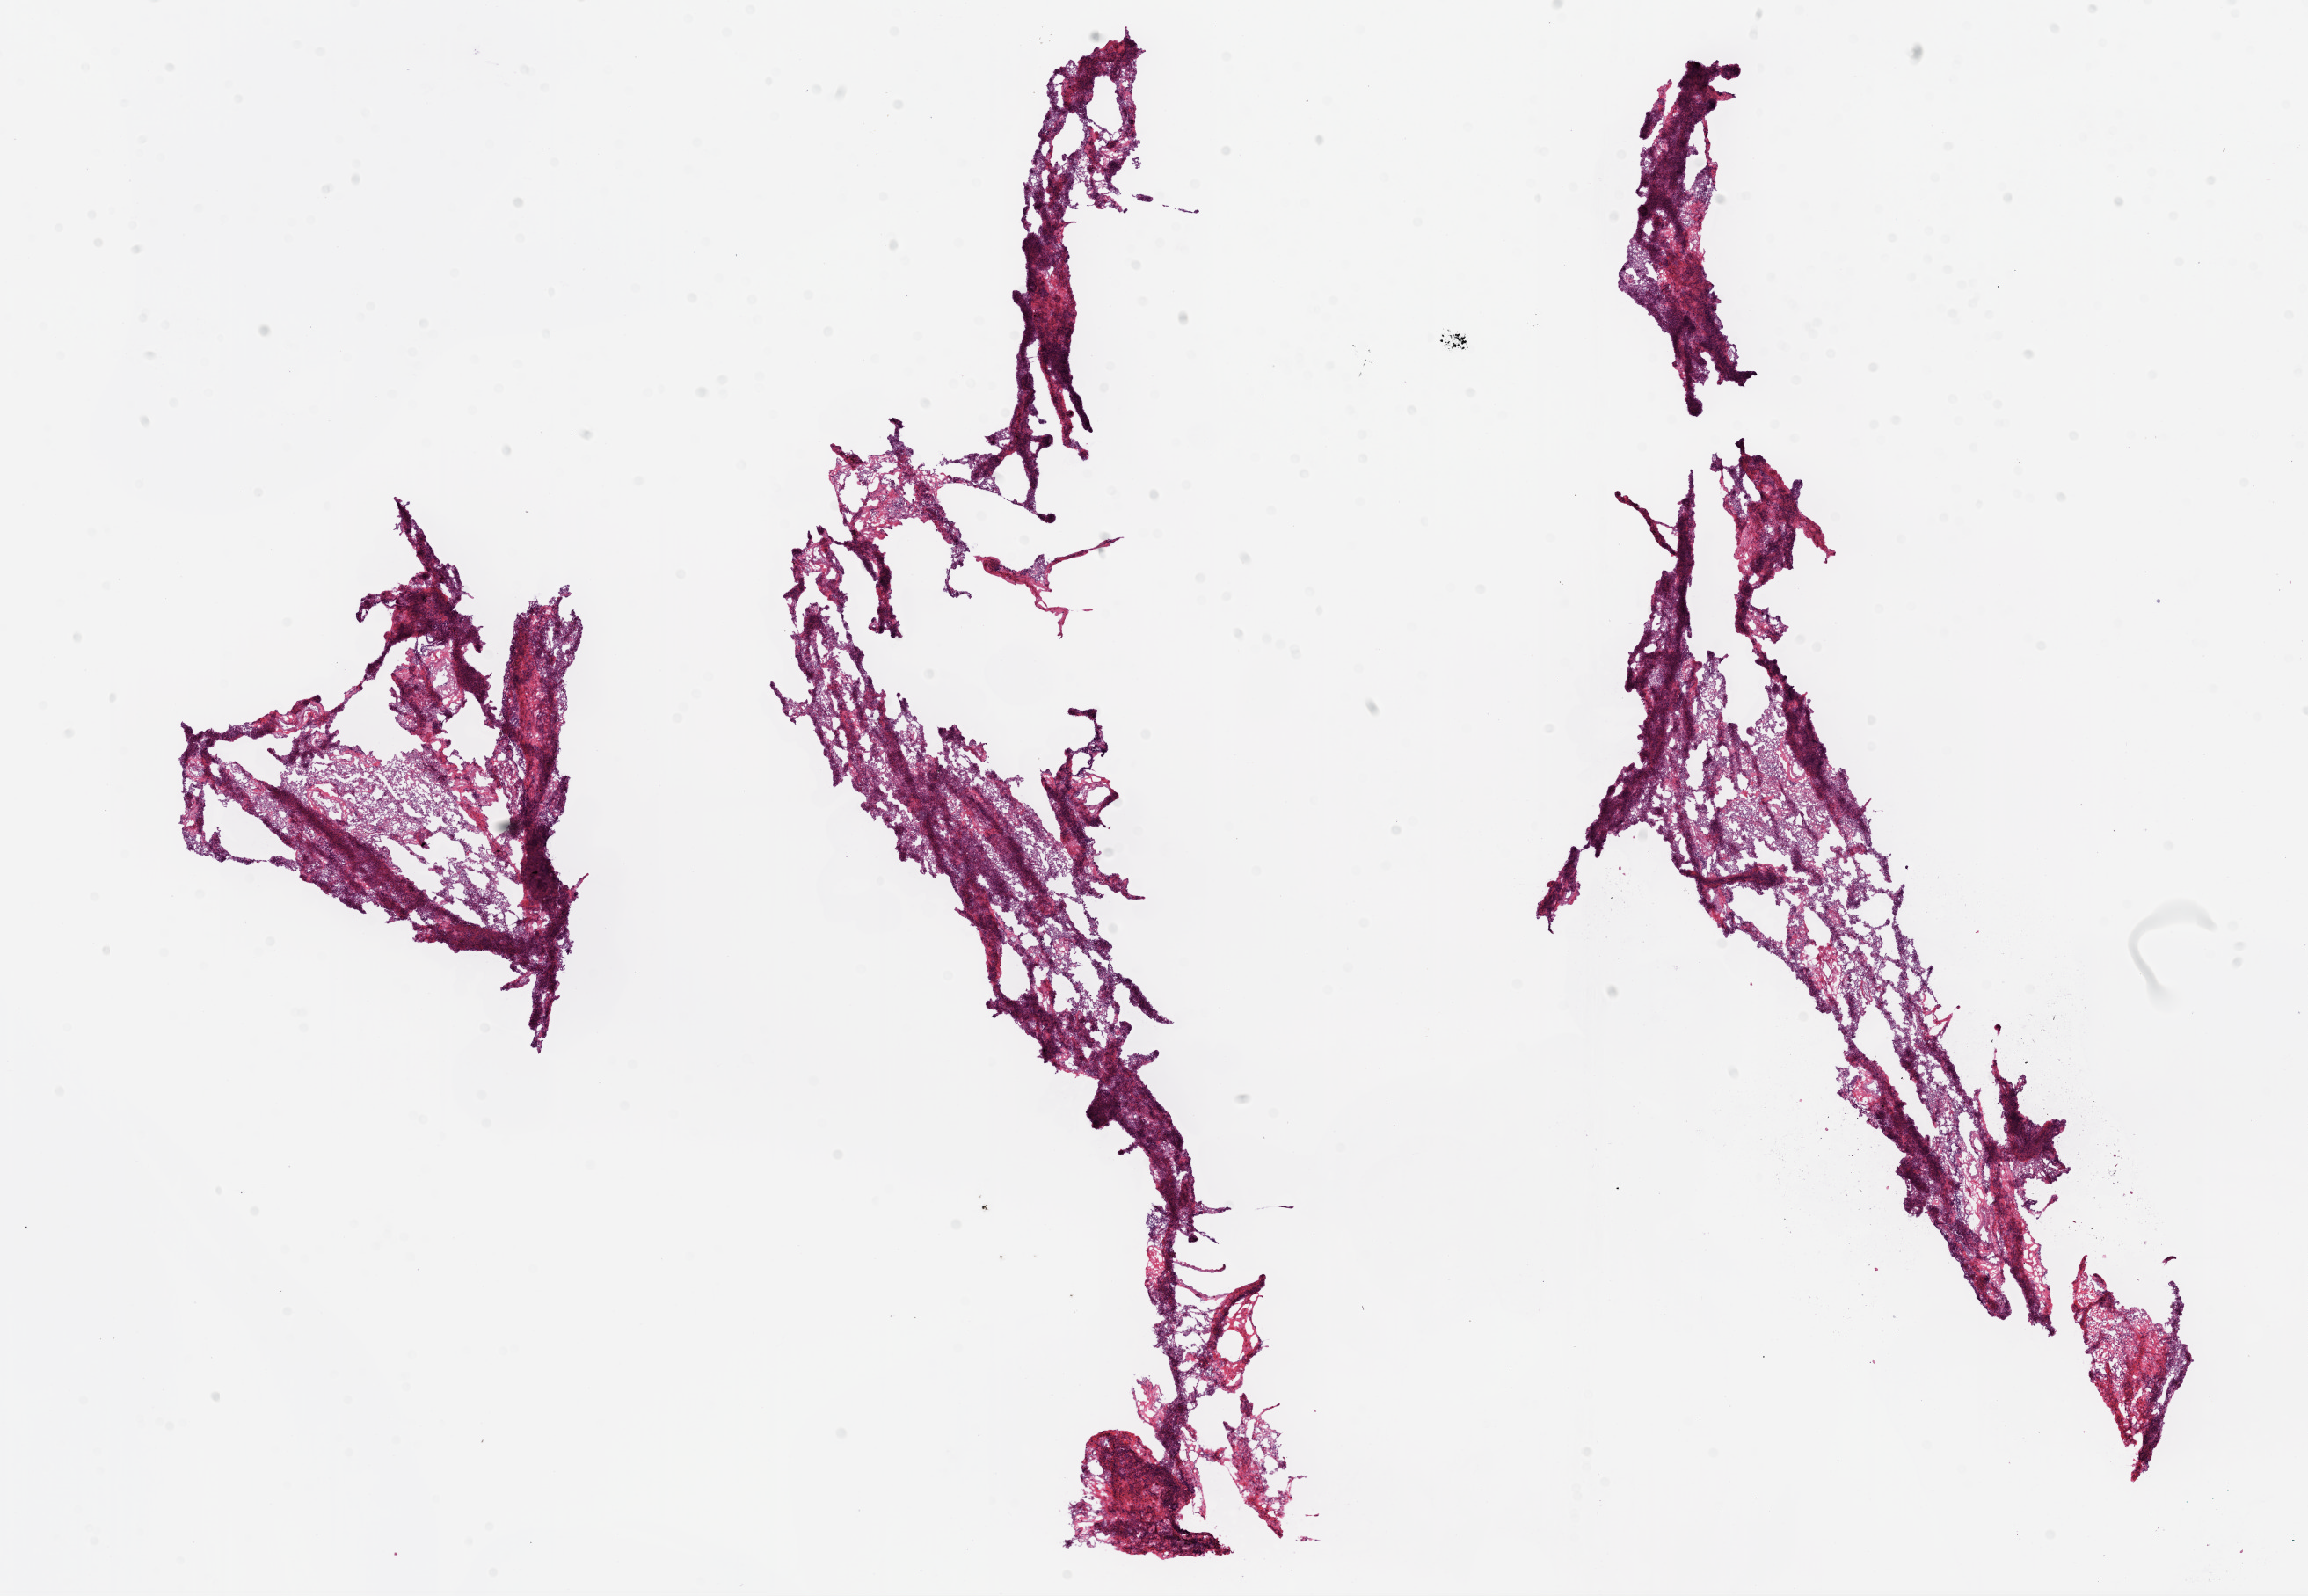
Digitized Hematoxylin and eosin (H&E) stained tissue section (whole slide) — shown as a low-resolution overview of the whole scanned area (about 21.1 x 14.6 mm, from a 20x scan); frozen section from the bottom of the tissue portion; sample: solid tissue normal (non-tumour tissue), lung. Male, age 62 years at initial diagnosis.
- this section: solid tissue normal (non-tumour) sample from the same patient
- patient diagnosis: Squamous cell carcinoma, NOS (lower lobe, lung)